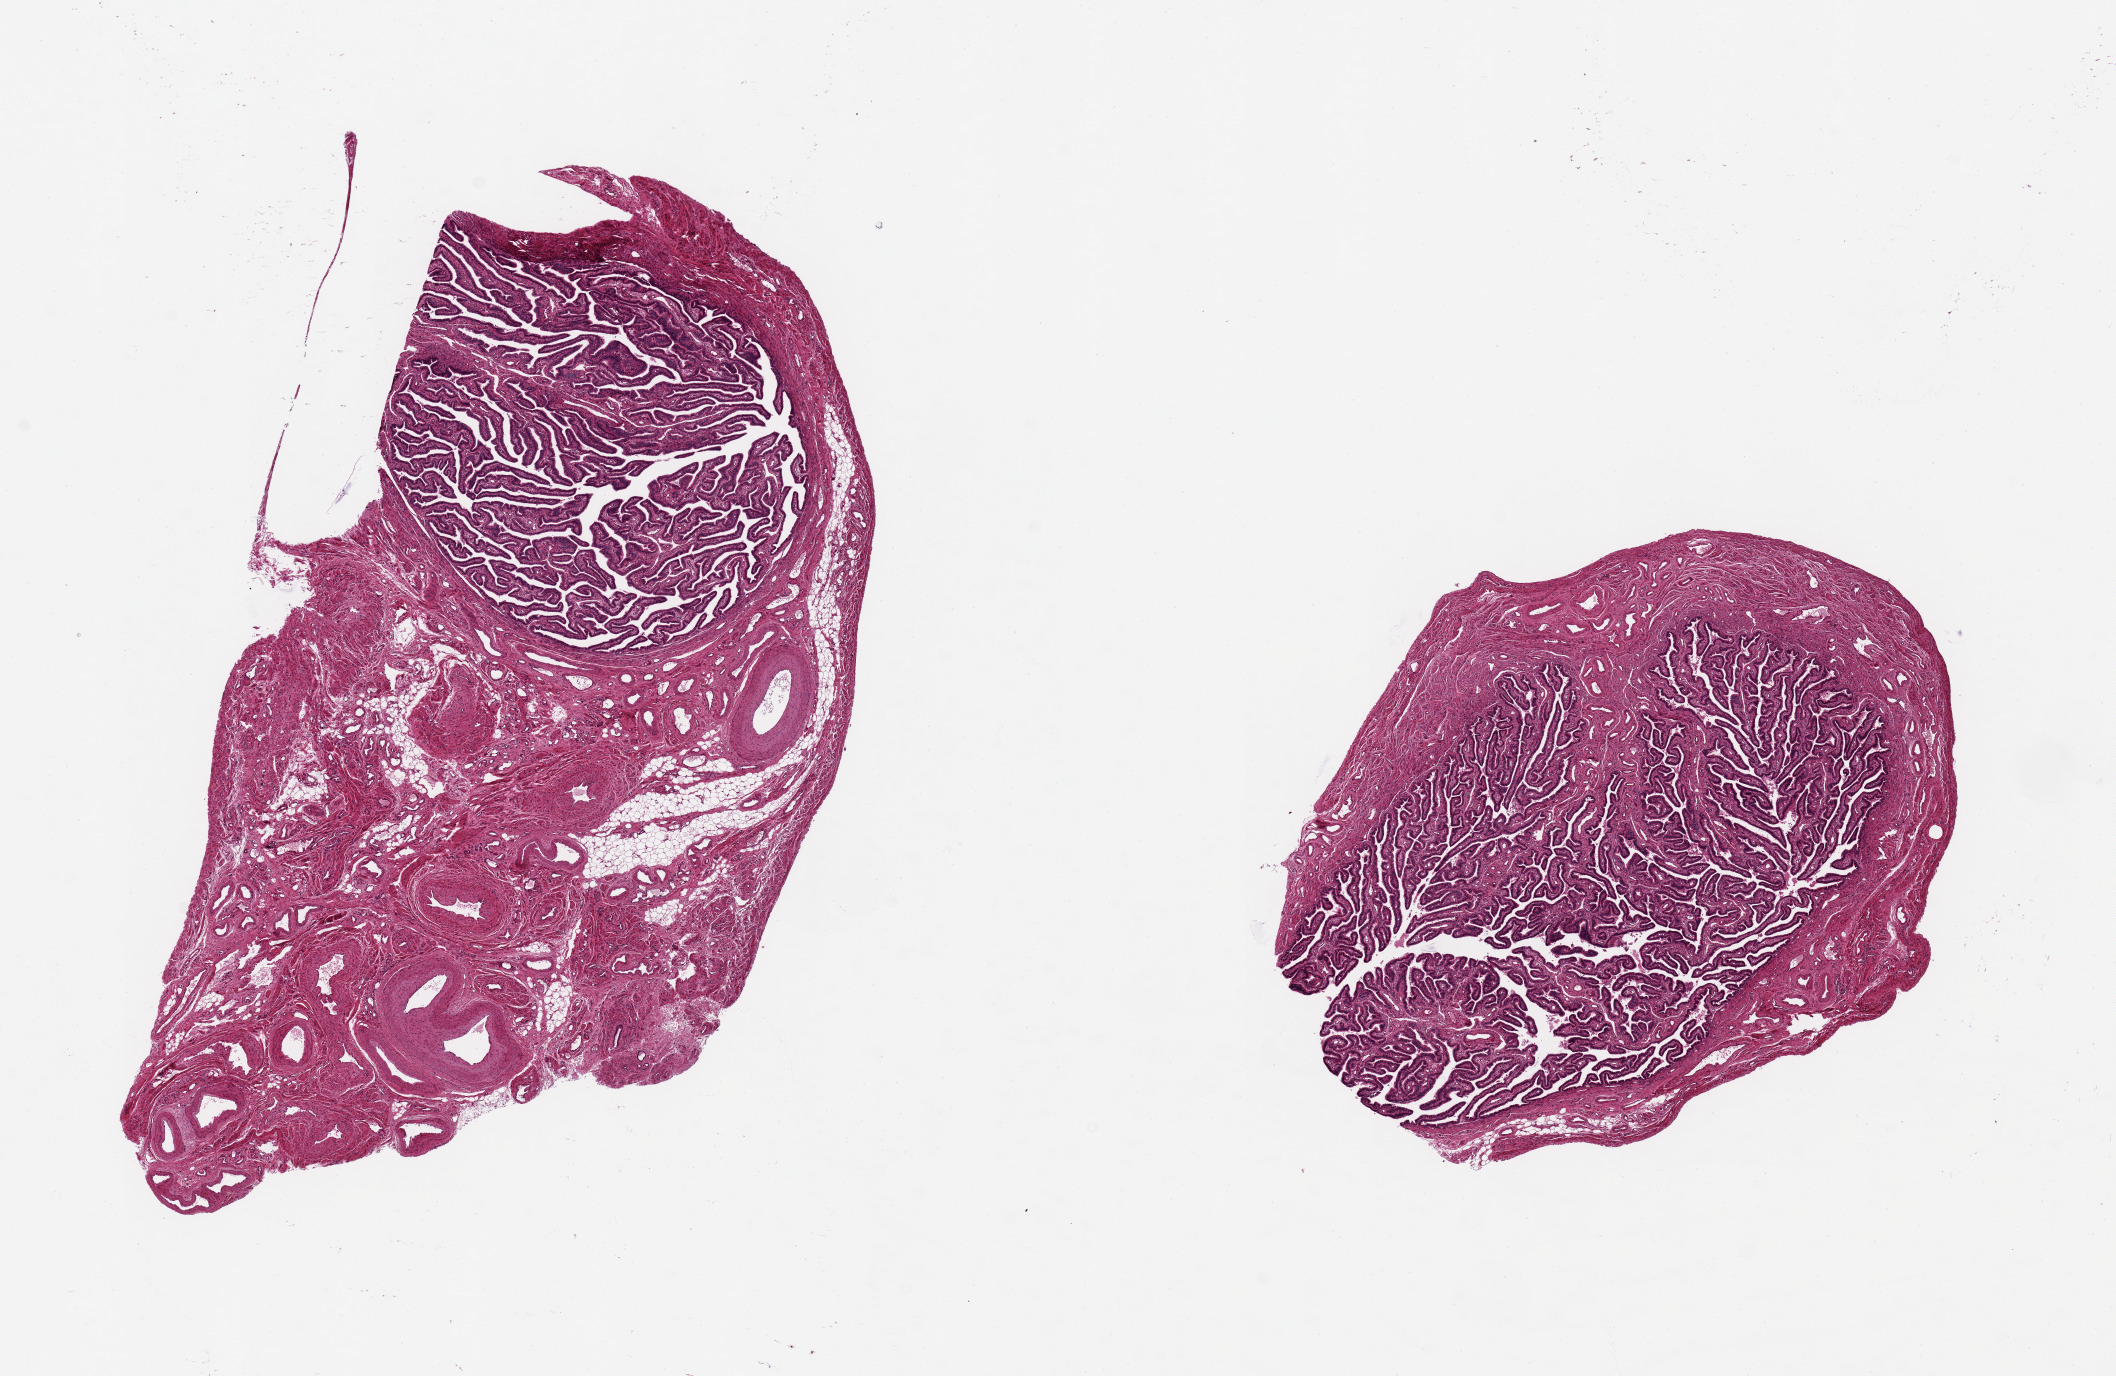
Haematoxylin and eosin whole-slide image — whole scanned area (about 16.7 x 10.9 mm, slide scanned at 20x) shown as a low-resolution overview. PAXgene-fixed paraffin-embedded (PFPE) section. Target tissue: fallopian tube. Tissue donor sample.
• reviewer comment on this tissue sample: 2 pieces 9x4 & 6x5 mm;; very good fimbriated specimens; one has ~60% vascularized fibroadipose stroma at one end; other has <10% surrounding stroma